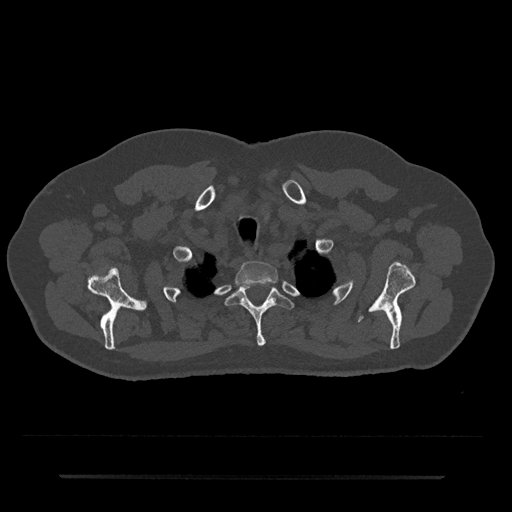
CT including the spine, one axial slice. Position 614 of 797 along the scan axis. 120 kVp. Bone window (W 1800 / L 400 HU). 512 × 512 image matrix. Male patient, age 69 years. Case-level facts recorded for this patient, not image findings: primary cancer: prostate.
Annotated regions visible in this slice (semi-automatic segmentation, software-assisted and operator-edited):
- T1 vertebra: box from (x=235, y=261) to (x=278, y=285) px
- T2 vertebra: (x=225, y=280)–(x=295, y=346)